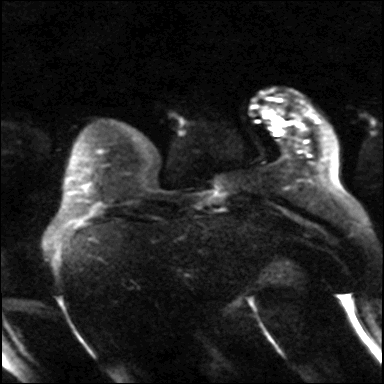
Breast MRI, one axial slice; position 6 of 36 along the scan axis; diffusion-weighted series; image 2 of 4 stored at this slice position (different b-values; order by instance number); 3 T; 4 mm slice thickness; 384 × 384 image matrix, field of view 320 × 320 mm. Female patient.
Structures marked on this image (expert manual segmentation):
- tumour on diffusion-weighted imaging: bounding box (x1, y1, x2, y2) in pixels: (275, 118, 279, 125)